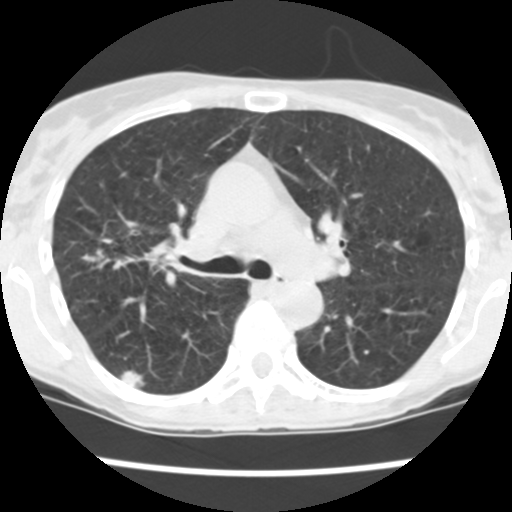
Low-dose screening chest CT, one axial slice. Position 156 of 252 along the scan axis. Reconstruction kernel STANDARD. Lung window (W 1500 / L -600 HU). 2.5 mm slice thickness. 512 × 512 image matrix, field of view 276 × 276 mm.
Annotated regions visible in this slice (expert manual segmentation):
- lesion 1 (tumor, upper lobe of right lung): box from (x=120, y=371) to (x=145, y=387) px
- lesion 2 (tumor, lower lobe of right lung): (x=147, y=240)–(x=170, y=263)